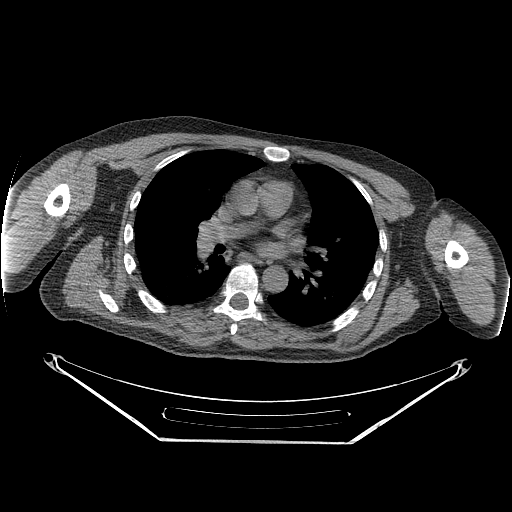
CT of an extremity soft-tissue mass (from a PET/CT study), one axial slice; slice 174 of 267 in the series (ordered by position); soft-tissue window (W 400 / L 40 HU); 3.75 mm slice thickness; 512 × 512 image matrix, field of view 500 × 500 mm. Male patient. From the clinical record (not read from this slice): histological type: pleiomorphic spindle cell undifferentiated; grade: high; site of the primary tumour: right parascapusular.
Outlined on this slice (expert contour drawn on MRI and transferred to this co-registered scan by the dataset authors):
- gross tumour volume including surrounding oedema: bounding box [x1, y1, x2, y2] px = [164, 315, 204, 328]